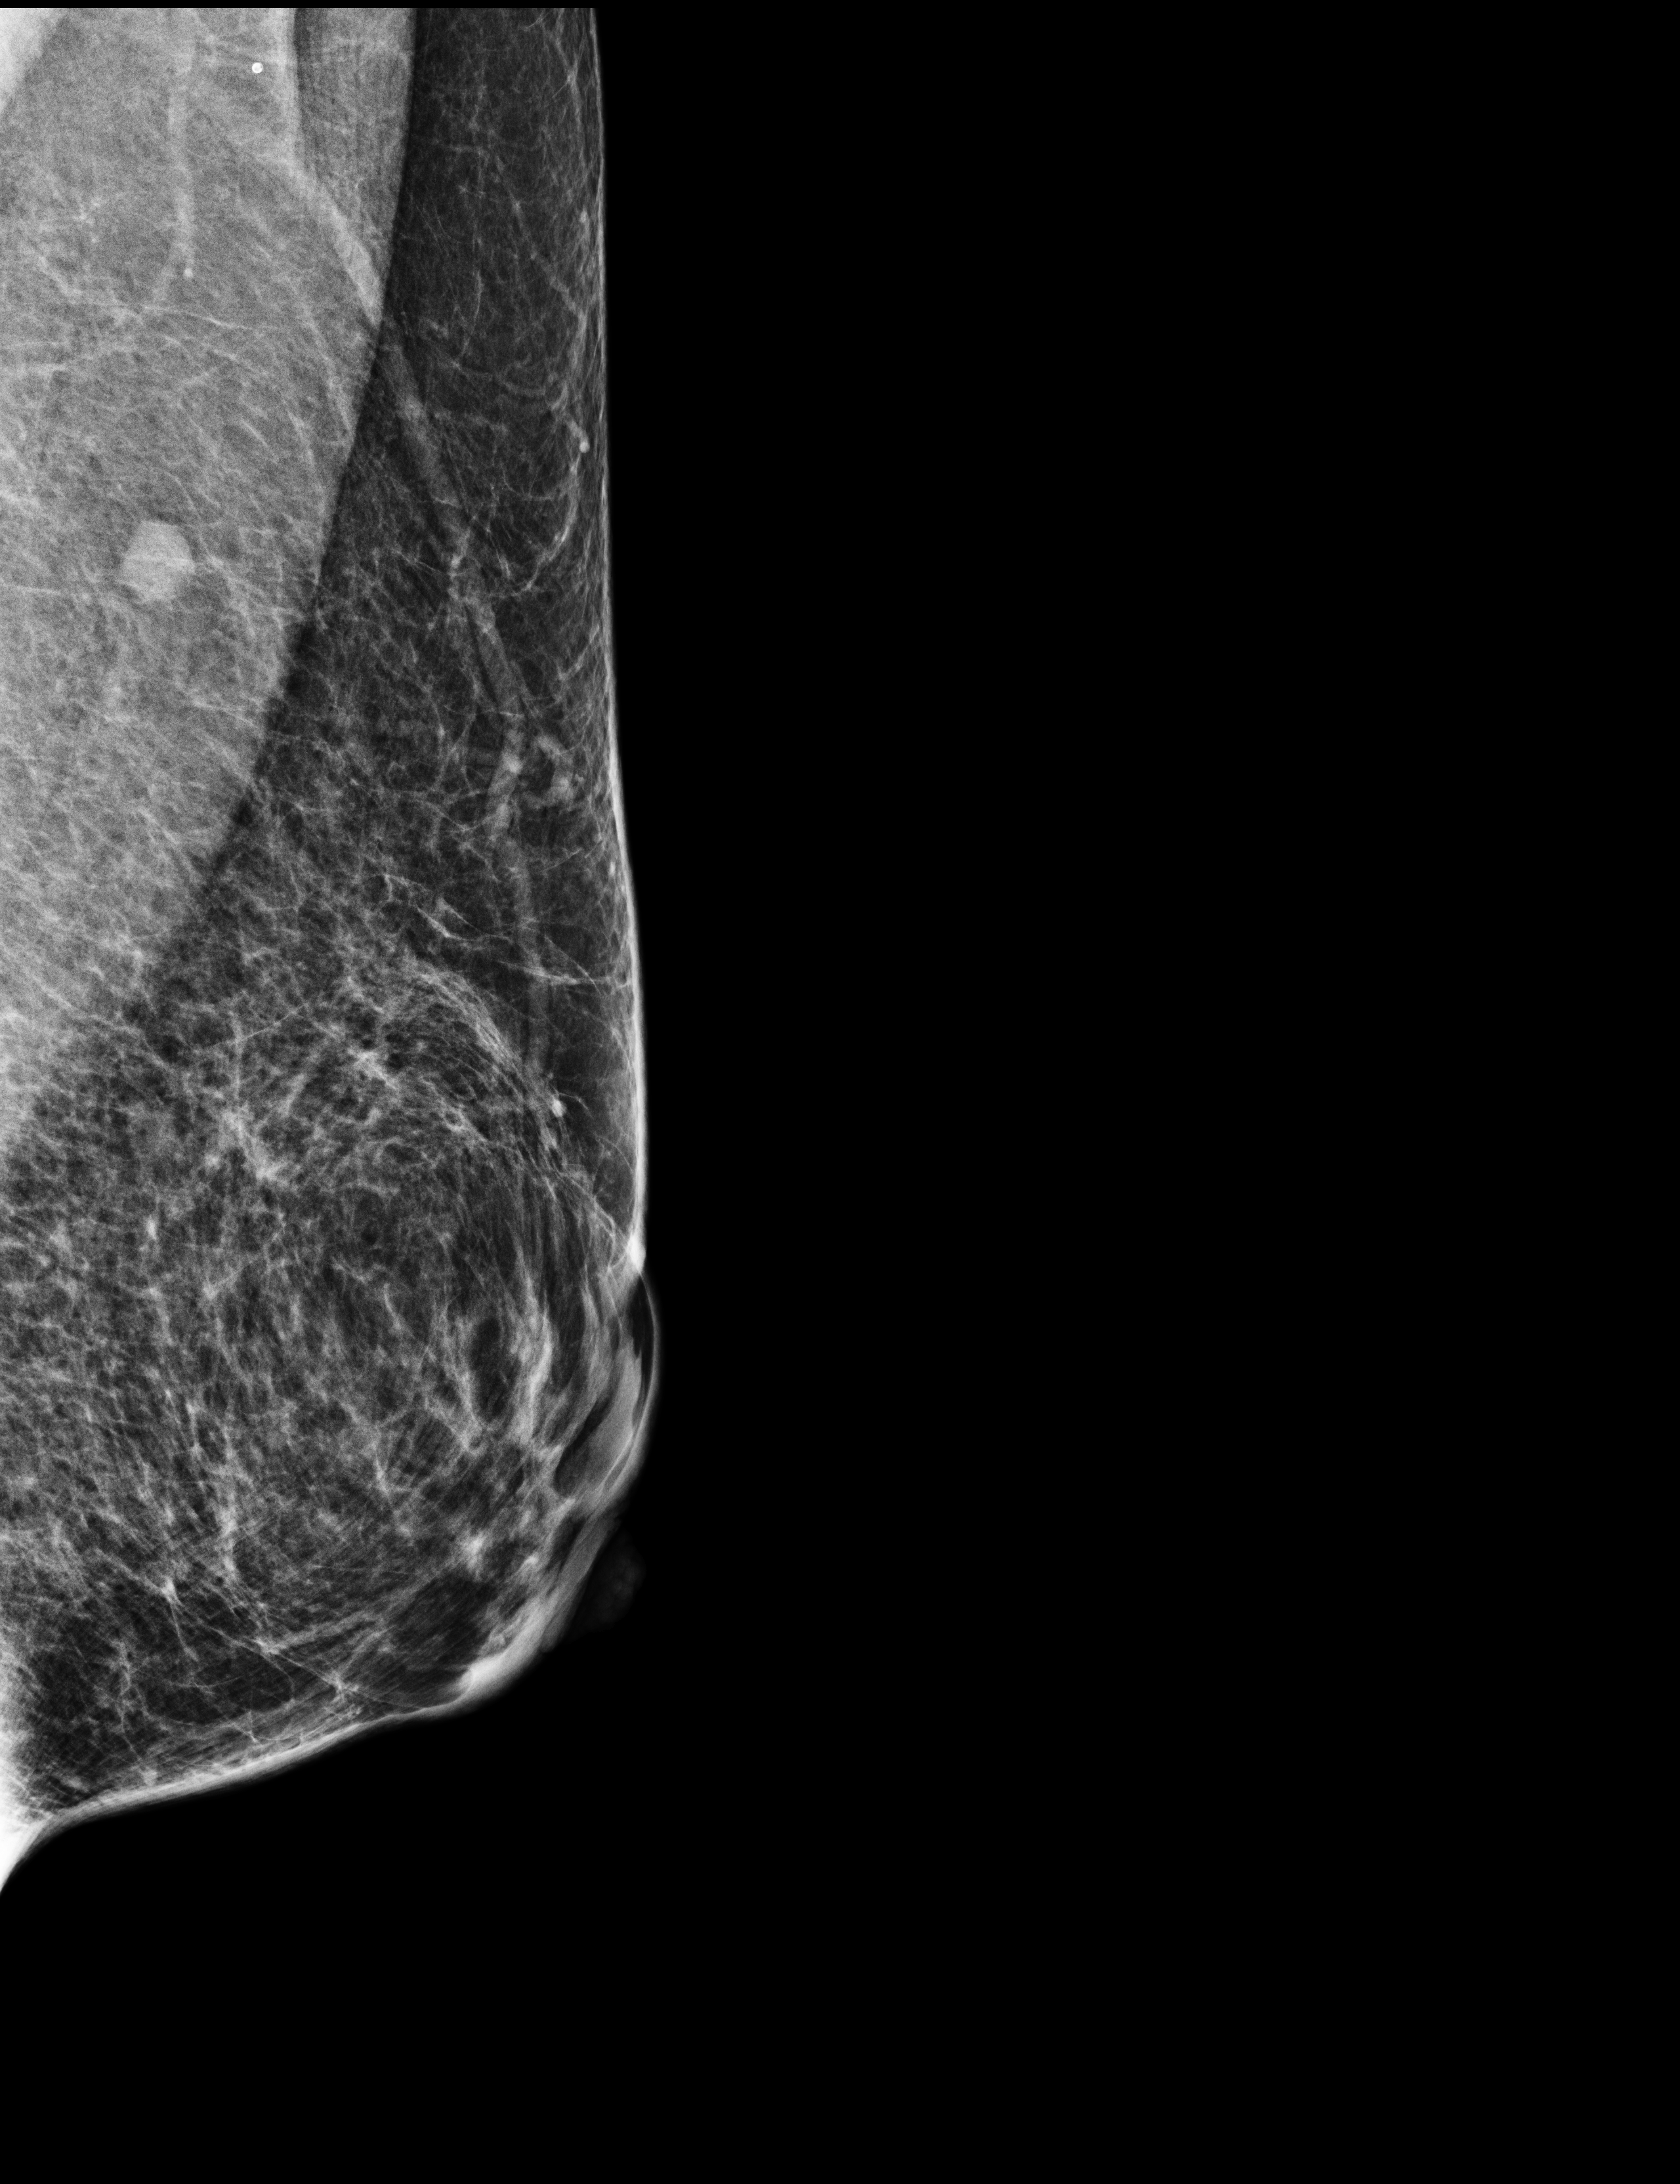
Digital mammogram (FFDM), left breast, MLO view, annual screening mammography examination, system: Selenia Dimensions. Patient aged 51 years (female).
BI-RADS breast density category at the screening exam (both breasts, scale 1–4): 3. Final BI-RADS assessment for this screening round (tomosynthesis exam, both breasts): category 2. Recall: no recall after this screen.